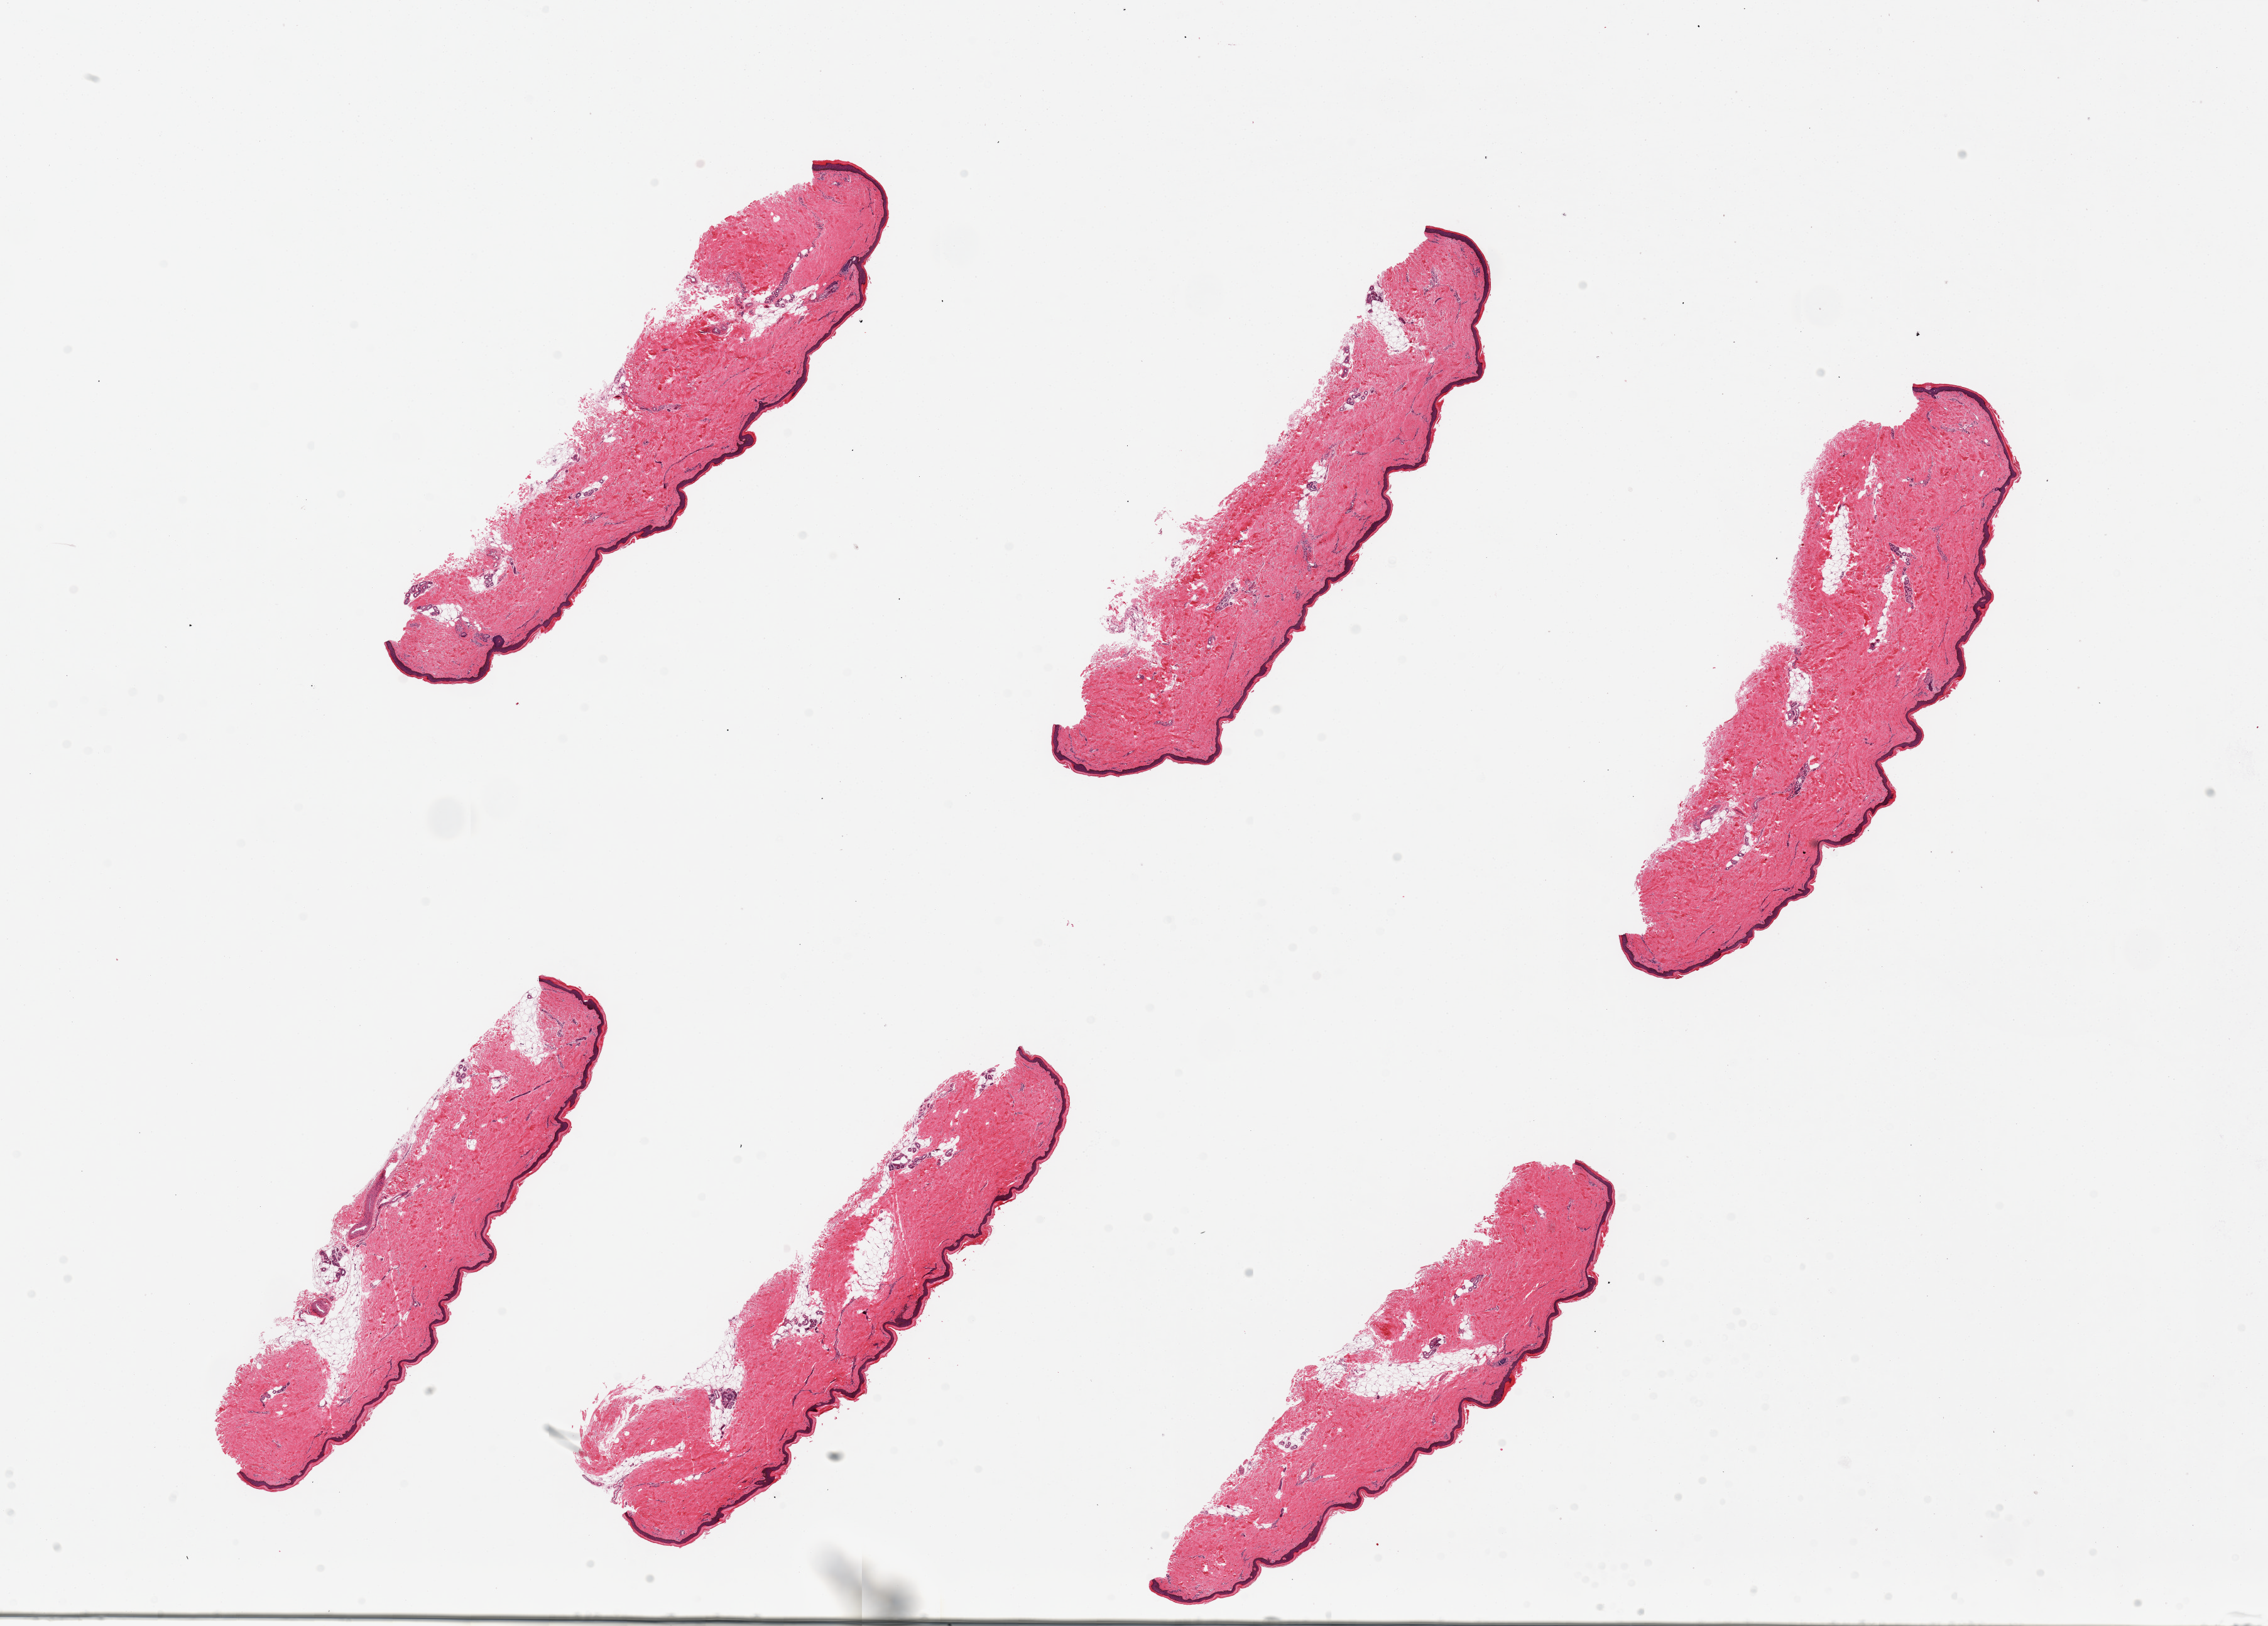
Digitized haematoxylin and eosin-stained section, whole scanned area (about 28.5 x 20.5 mm, acquisition: 20x scan) shown as a low-resolution overview. PAXgene-fixed, paraffin-embedded tissue. Sampled site (target tissue): skin of lower leg. Donor tissue sample.
Reviewer comment on this tissue sample: 6 pieces, up to 9x2mm. Well trimmed, but with 10-20% intradermal adipose.